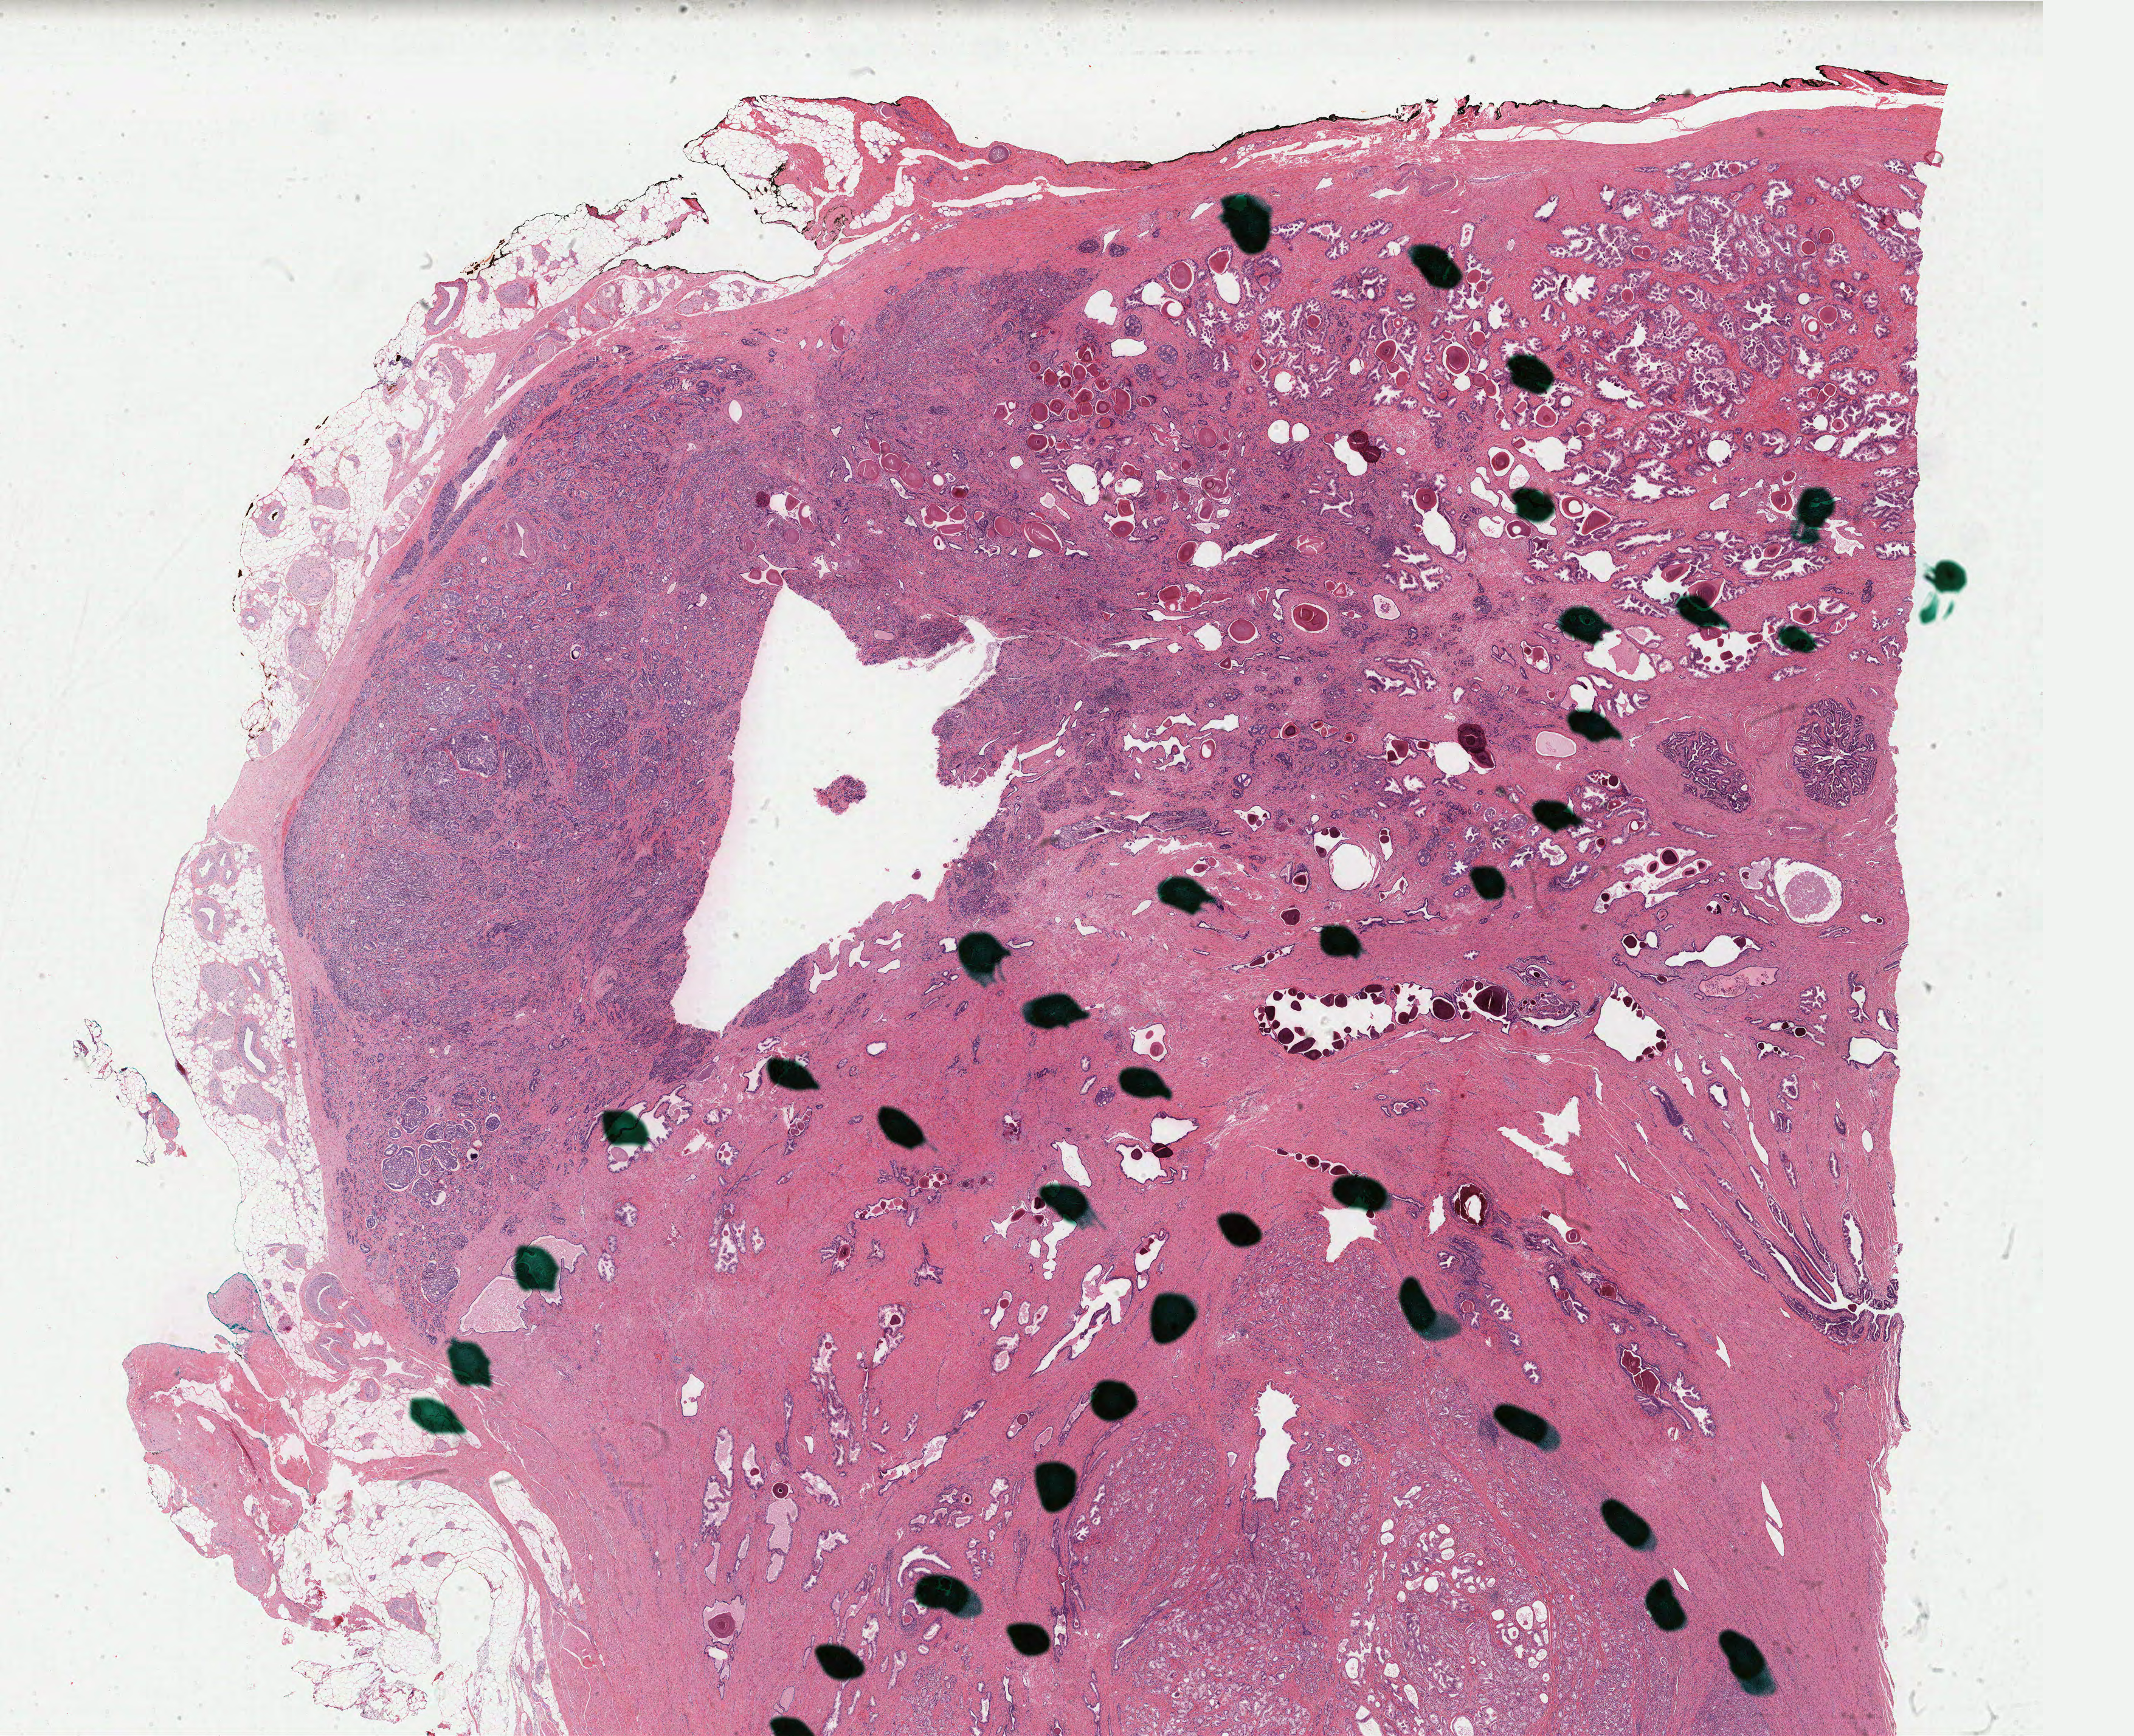
Whole-slide histology image, Hematoxylin and eosin (H&E) stained — whole scanned area (about 27.9 x 22.7 mm) shown as a low-resolution overview; FFPE section; primary tumour sample from the prostate. Male, age 64 years at initial diagnosis. Gleason score: 7 (4+3).
Diagnosis: Adenocarcinoma, NOS (prostate gland). Laterality: left. Lymph nodes positive (case pathology): 1 of 15 examined.